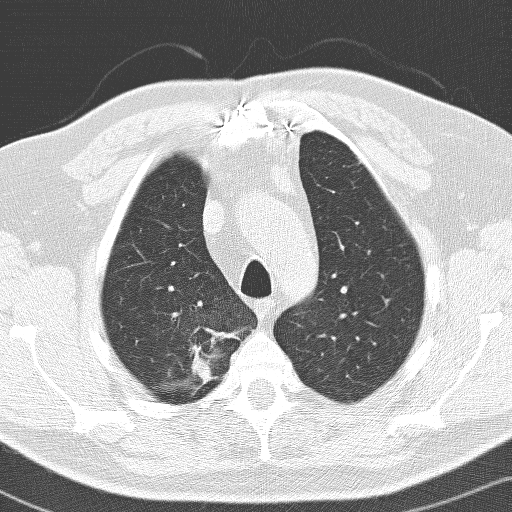
Low-dose screening chest CT, one axial slice. Position 116 of 141 along the scan axis. 120 kVp. Lung window (W 1500 / L -600 HU). 3.2 mm slice thickness. 512 × 512 image matrix, field of view 326 × 326 mm.
Outlined on this slice (outlined manually by an expert reader):
- lesion 1 (tumor, upper lobe of right lung): box from (x=192, y=339) to (x=214, y=390) px